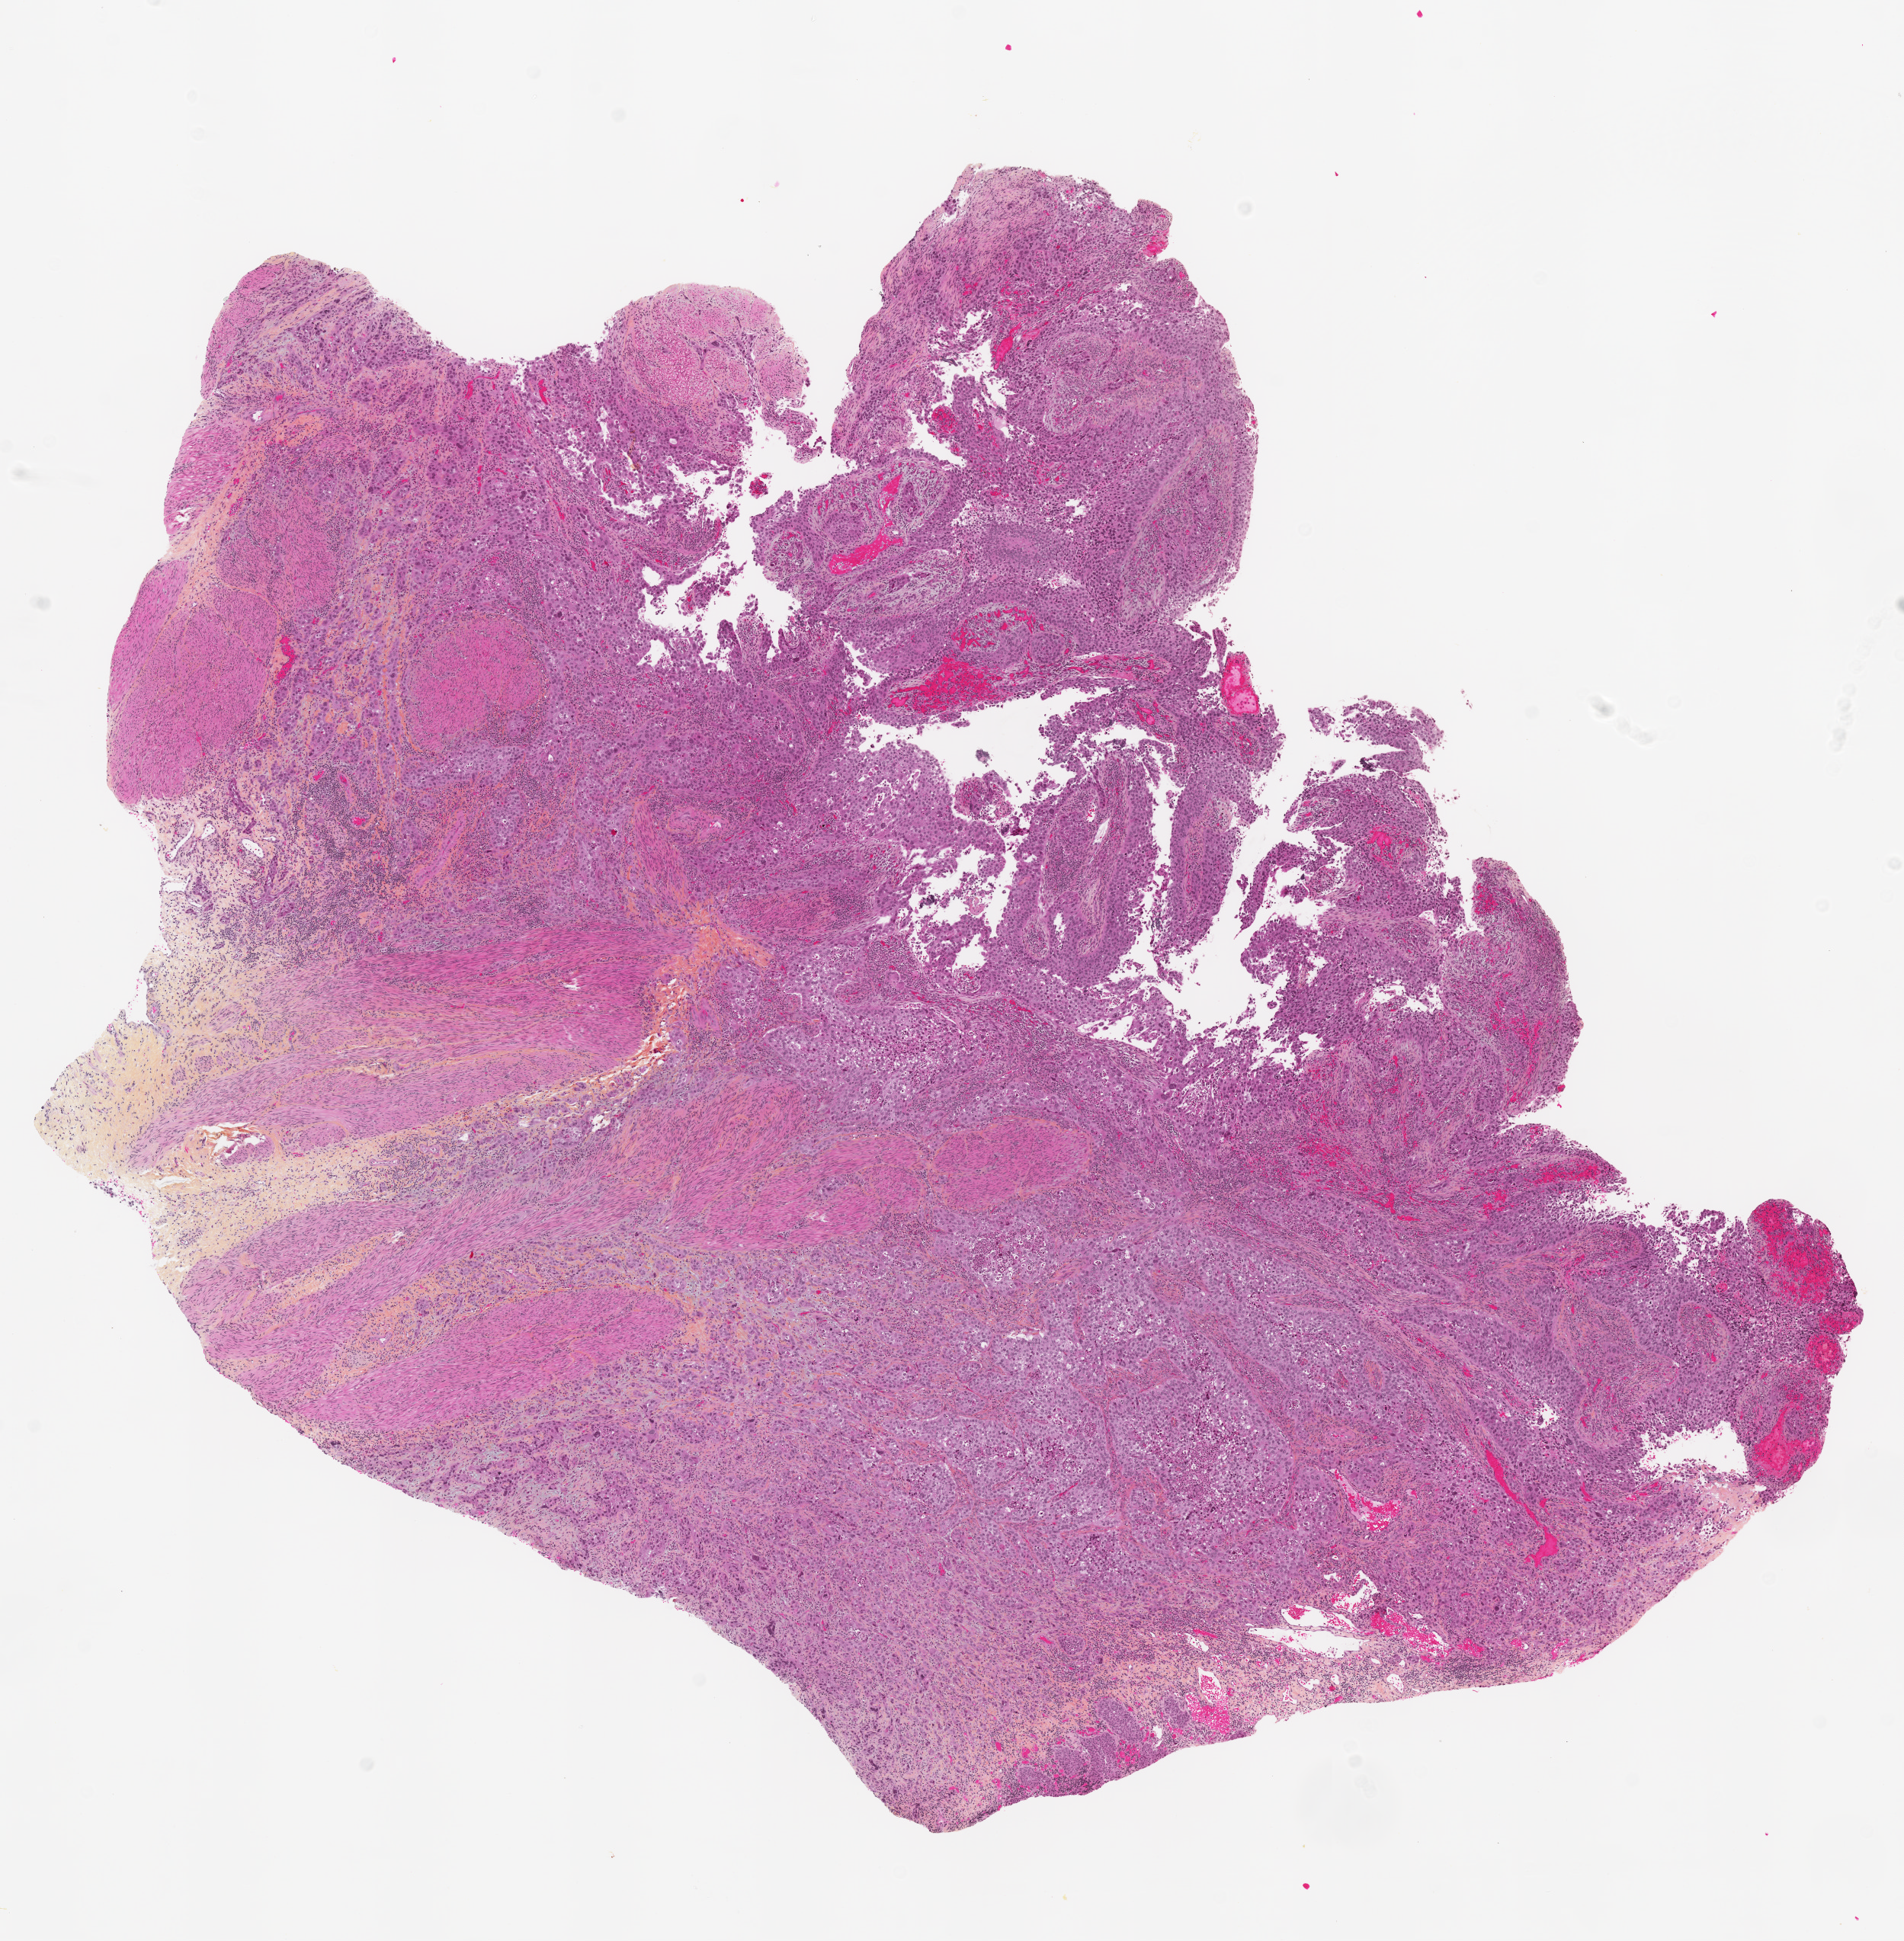
Digitized Hematoxylin and eosin (H&E) stained tissue section (whole slide) — shown as a low-resolution overview of the whole scanned area (about 10.0 x 10.2 mm, acquisition: 20x scan). Formalin-fixed paraffin-embedded (FFPE) diagnostic section. Sample: primary tumour, bladder. Patient: male, age at initial diagnosis 56 years. Histologic grade: high grade.
* diagnosis: Transitional cell carcinoma
* TNM: T3 N0 M0
* lymph nodes positive (case pathology): 0 of 5 examined
* AJCC pathologic stage: III (6th edition)